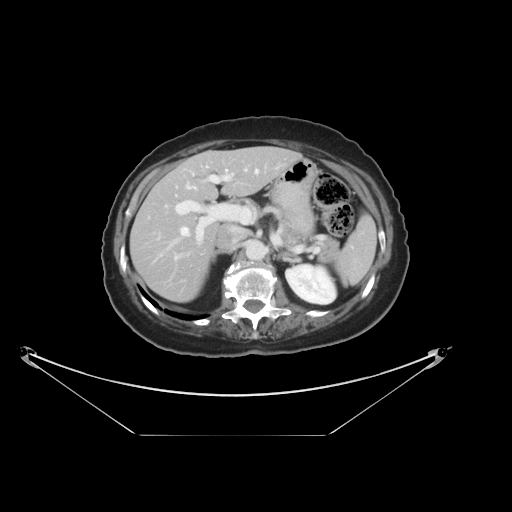
Contrast-enhanced abdominal CT, one axial slice; slice 21 of 36 in the series (ordered by position); 120 kVp; intravenous contrast given; soft-tissue window (W 400 / L 40 HU); 5 mm slice thickness; 512 × 512 image matrix. Female patient, age 70 years. From the clinical record (not read from this slice): diagnosis: colorectal cancer liver metastases, imaged before liver resection; multiple liver metastases: no; largest metastasis: 2.5 cm; chemotherapy before resection: no.
Structures marked on this image (expert manual segmentation):
- hepatic veins: box from (x=145, y=169) to (x=258, y=250) px
- liver: (x=132, y=148)–(x=300, y=302)
- planned liver remnant (the part of the liver to remain after resection): (x=132, y=148)–(x=300, y=302)
- portal vein (with intrahepatic branches): (x=164, y=168)–(x=247, y=261)